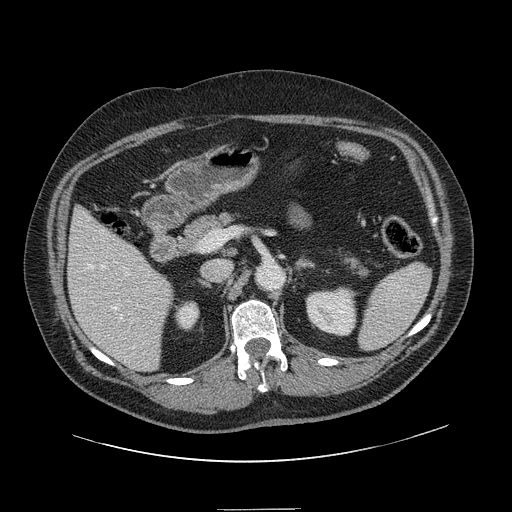
Contrast-enhanced abdominal CT, one axial slice; 120 kVp; intravenous contrast given; soft-tissue window (W 400 / L 40 HU); 512 × 512 image matrix, field of view 451 × 451 mm. Male patient, age 61 years. Case-level facts recorded for this patient, not image findings: diagnosis: colorectal cancer liver metastases, imaged before liver resection; multiple liver metastases: yes.
Annotated regions visible in this slice (outlined manually by an expert reader):
- hepatic veins: bounding box [x1, y1, x2, y2] px = [87, 264, 134, 349]
- liver: [69, 209, 172, 371]
- planned liver remnant (the part of the liver to remain after resection): [70, 209, 172, 366]
- portal vein (with intrahepatic branches): [130, 320, 132, 323]